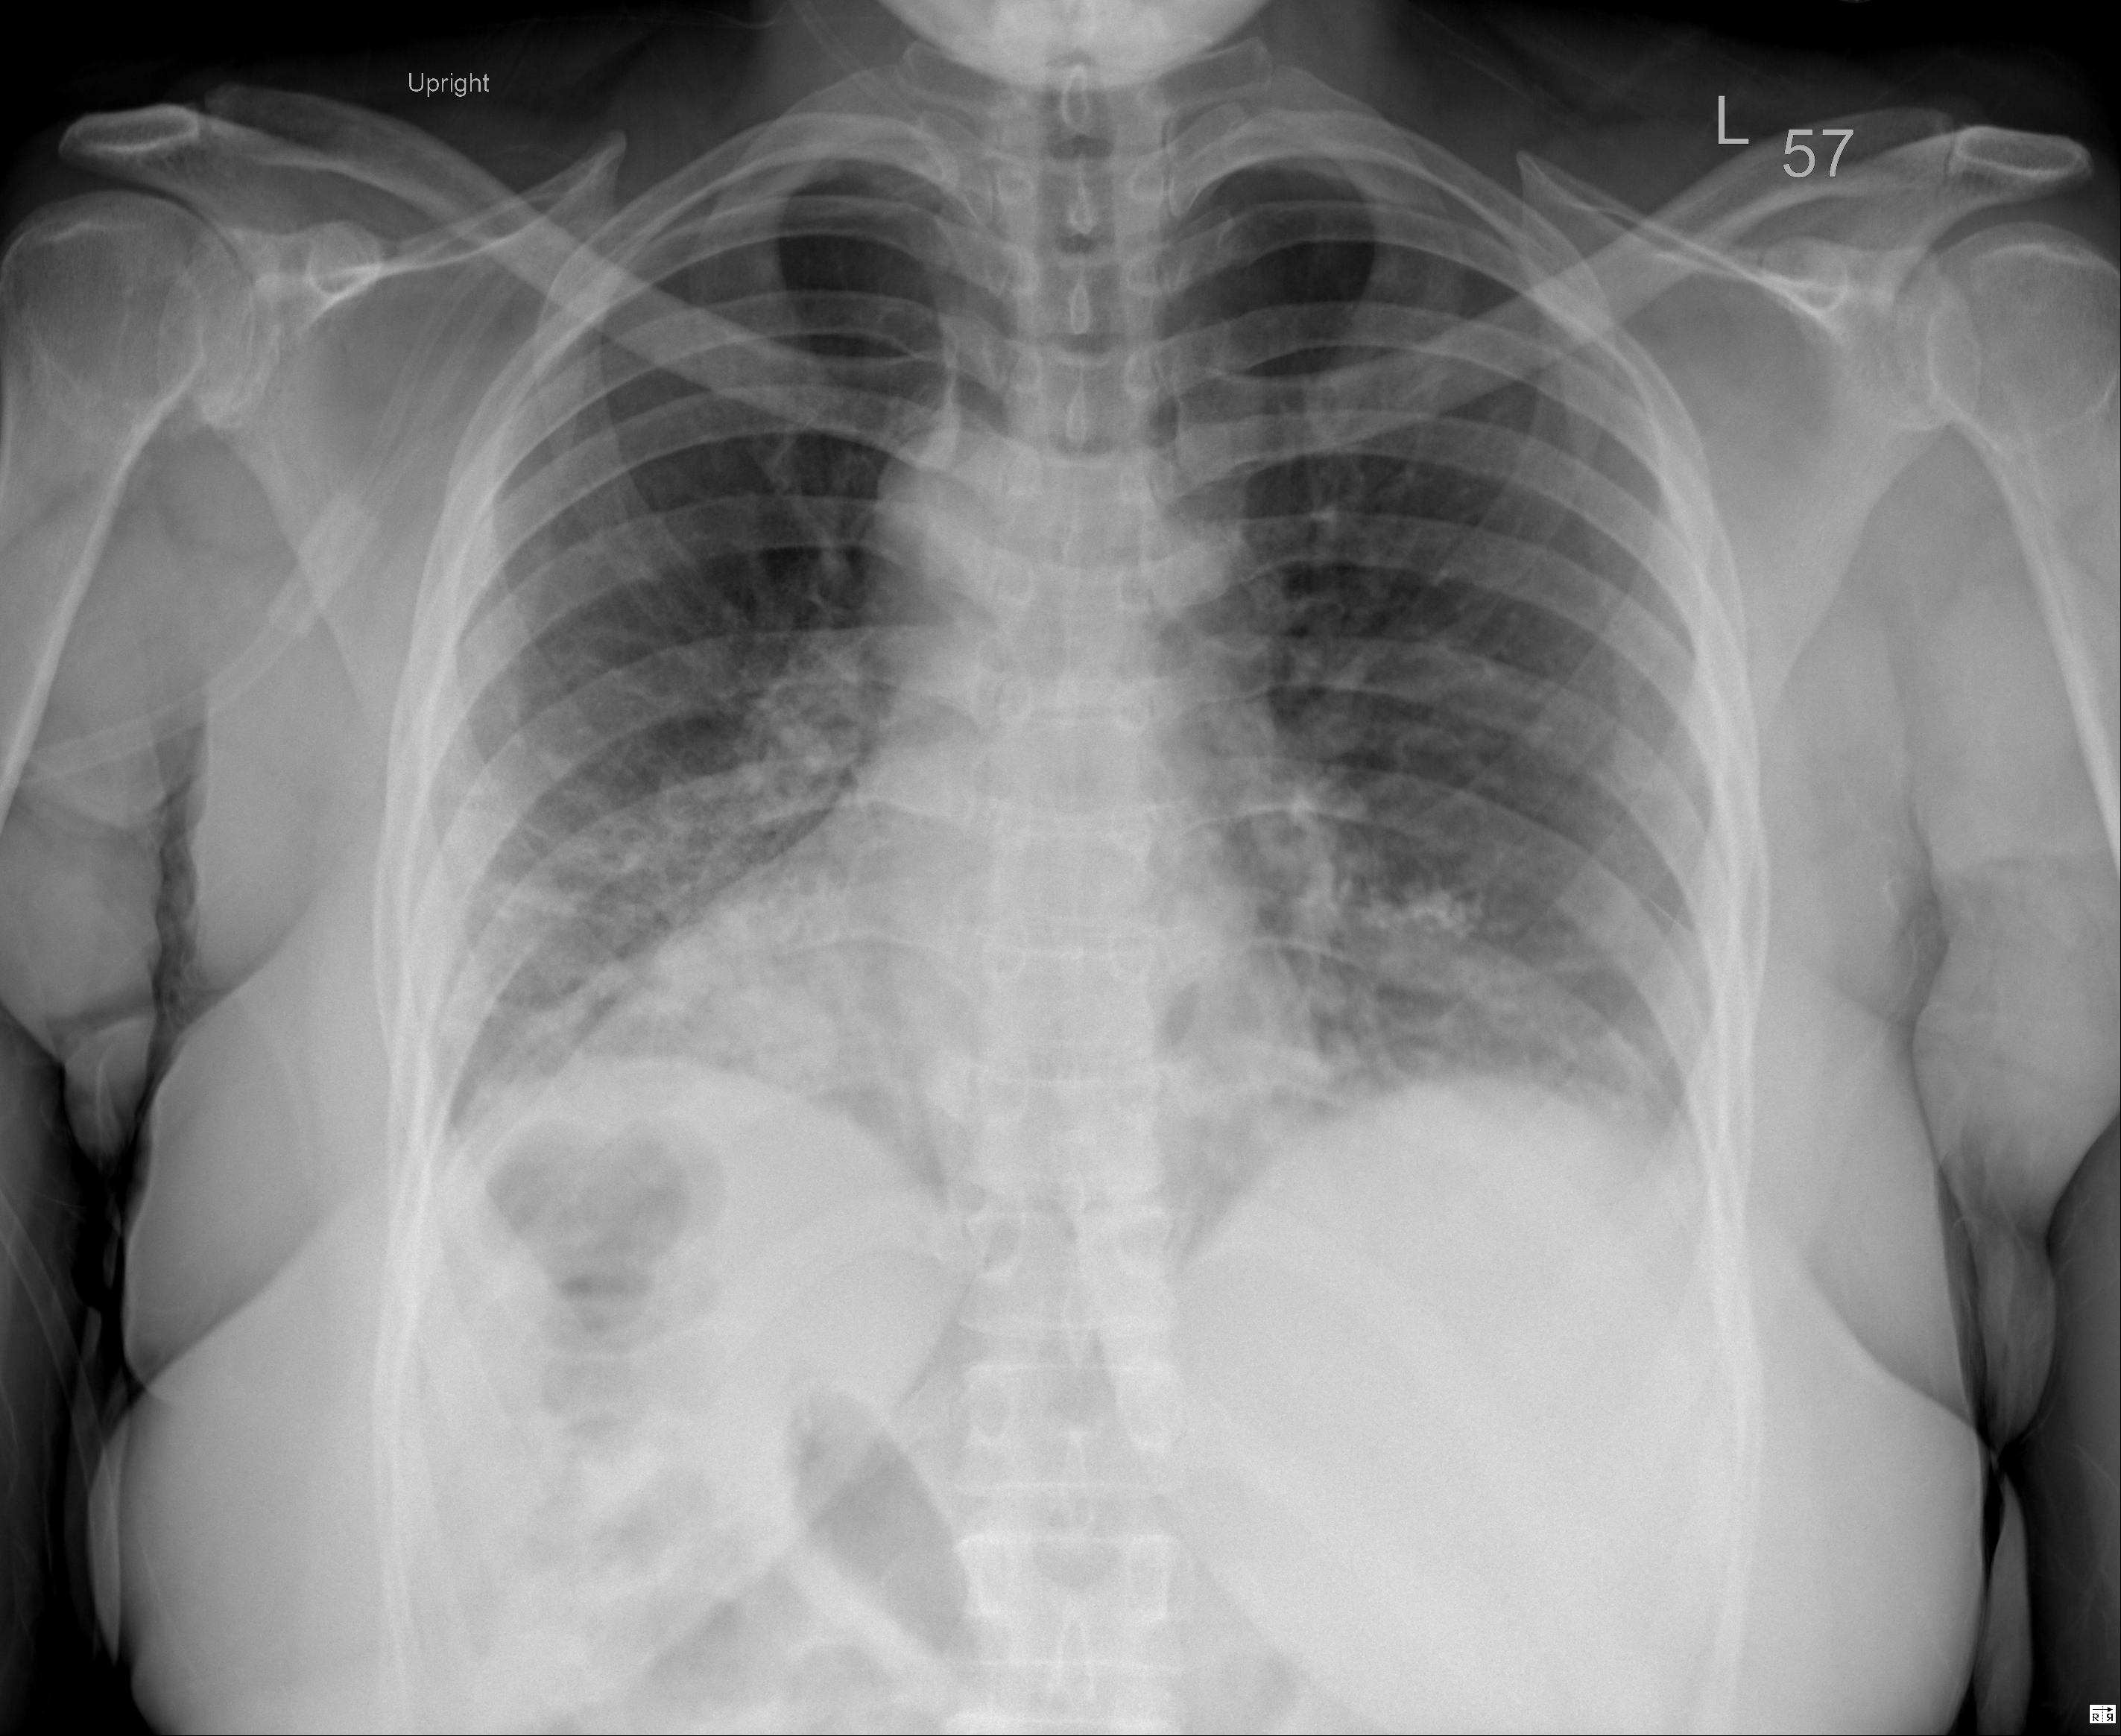
Chest X-ray, PA projection. Female patient, age 58 years; imaged 1 day after the COVID-19 diagnosis.
Key findings recorded by the radiologist: Patchy ill-defined airspace disease in both lung bases, little changed.